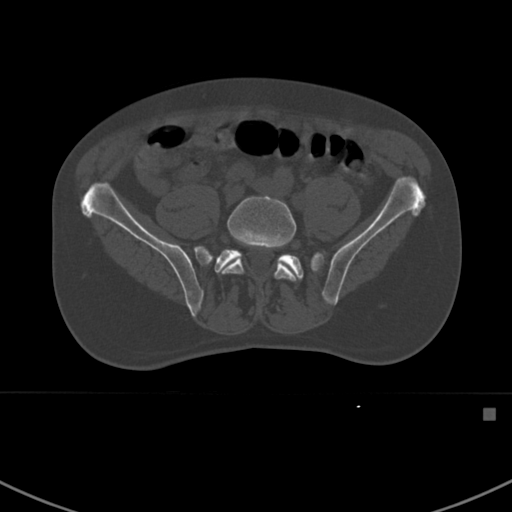
CT including the spine, one axial slice; position 213 of 412 along the scan axis; reconstruction kernel Br40s; bone window (W 1800 / L 400 HU); 512 × 512 image matrix, field of view 358 × 358 mm. Male patient, age 59 years. From the clinical record (not read from this slice): primary cancer: prostate.
Annotated regions visible in this slice (semi-automatic segmentation, software-assisted and operator-edited):
- L5 vertebra: bounding box [x1, y1, x2, y2] px = [222, 195, 300, 295]